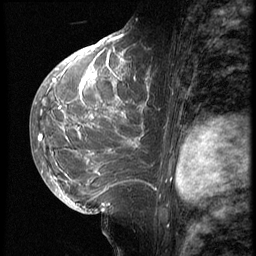
Breast MRI (dynamic contrast-enhanced), one sagittal slice. Position 35 of 62 along the scan axis. 3 images stored at this slice position (order not interpretable as contrast timing). 1.5 T. TE 4.2 ms, TR 9 ms. 2.5 mm slice thickness. 256 × 256 image matrix, field of view 180 × 180 mm. Female patient, age 28 years. Case-level facts recorded for this patient, not image findings: setting: breast cancer imaged before/during neoadjuvant chemotherapy.
Annotated regions visible in this slice (semi-automatic segmentation, software-assisted and operator-edited):
- analysis volume of interest (the breast-tissue region the enhancement analysis was run in; not a lesion): bounding box [x1, y1, x2, y2] px = [42, 45, 161, 207]
- tumour enhancement mask (voxels above the 140 % enhancement threshold inside the analysis volume of interest): [52, 48, 156, 191]